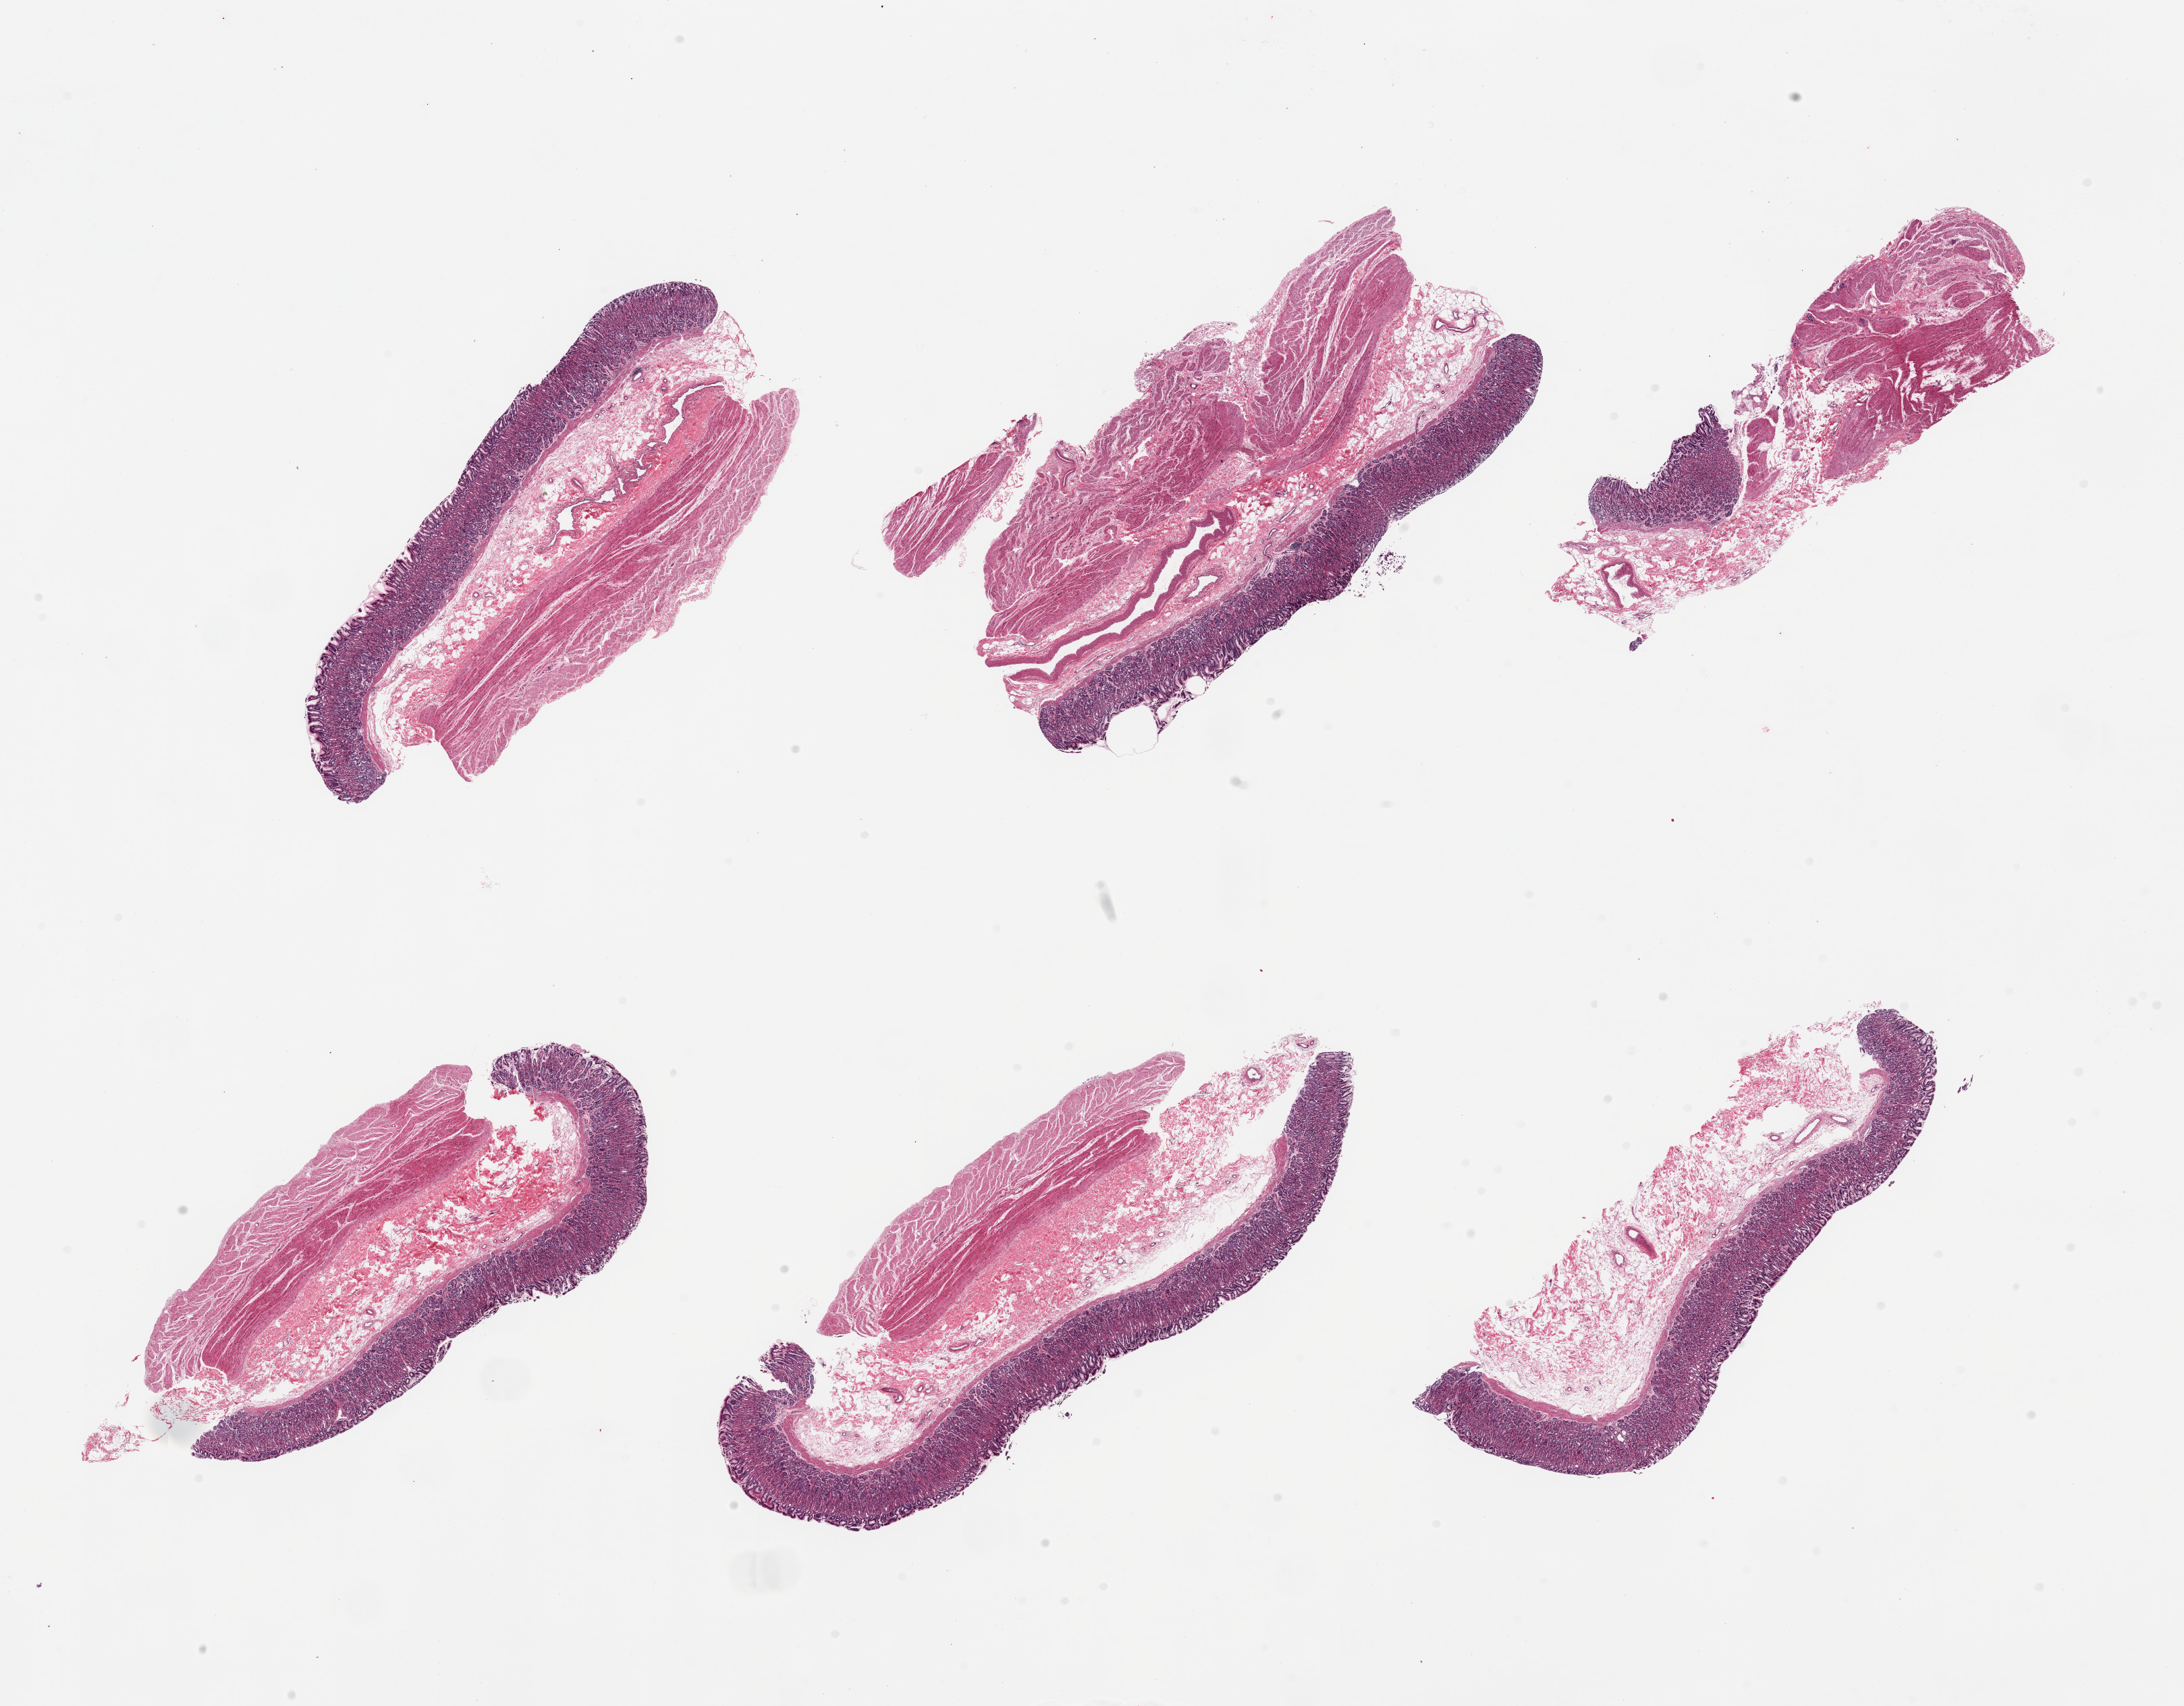
Whole-slide image, H&E stain, a low-resolution overview of the entire scanned area, about 25.6 x 20.0 mm; PAXgene-fixed paraffin-embedded (PFPE) section; section of stomach (target tissue); donor tissue sample. Female donor.
* reviewer comment on this tissue sample: 6 pieces; five are full thickness, one with mucosa/submucosa only